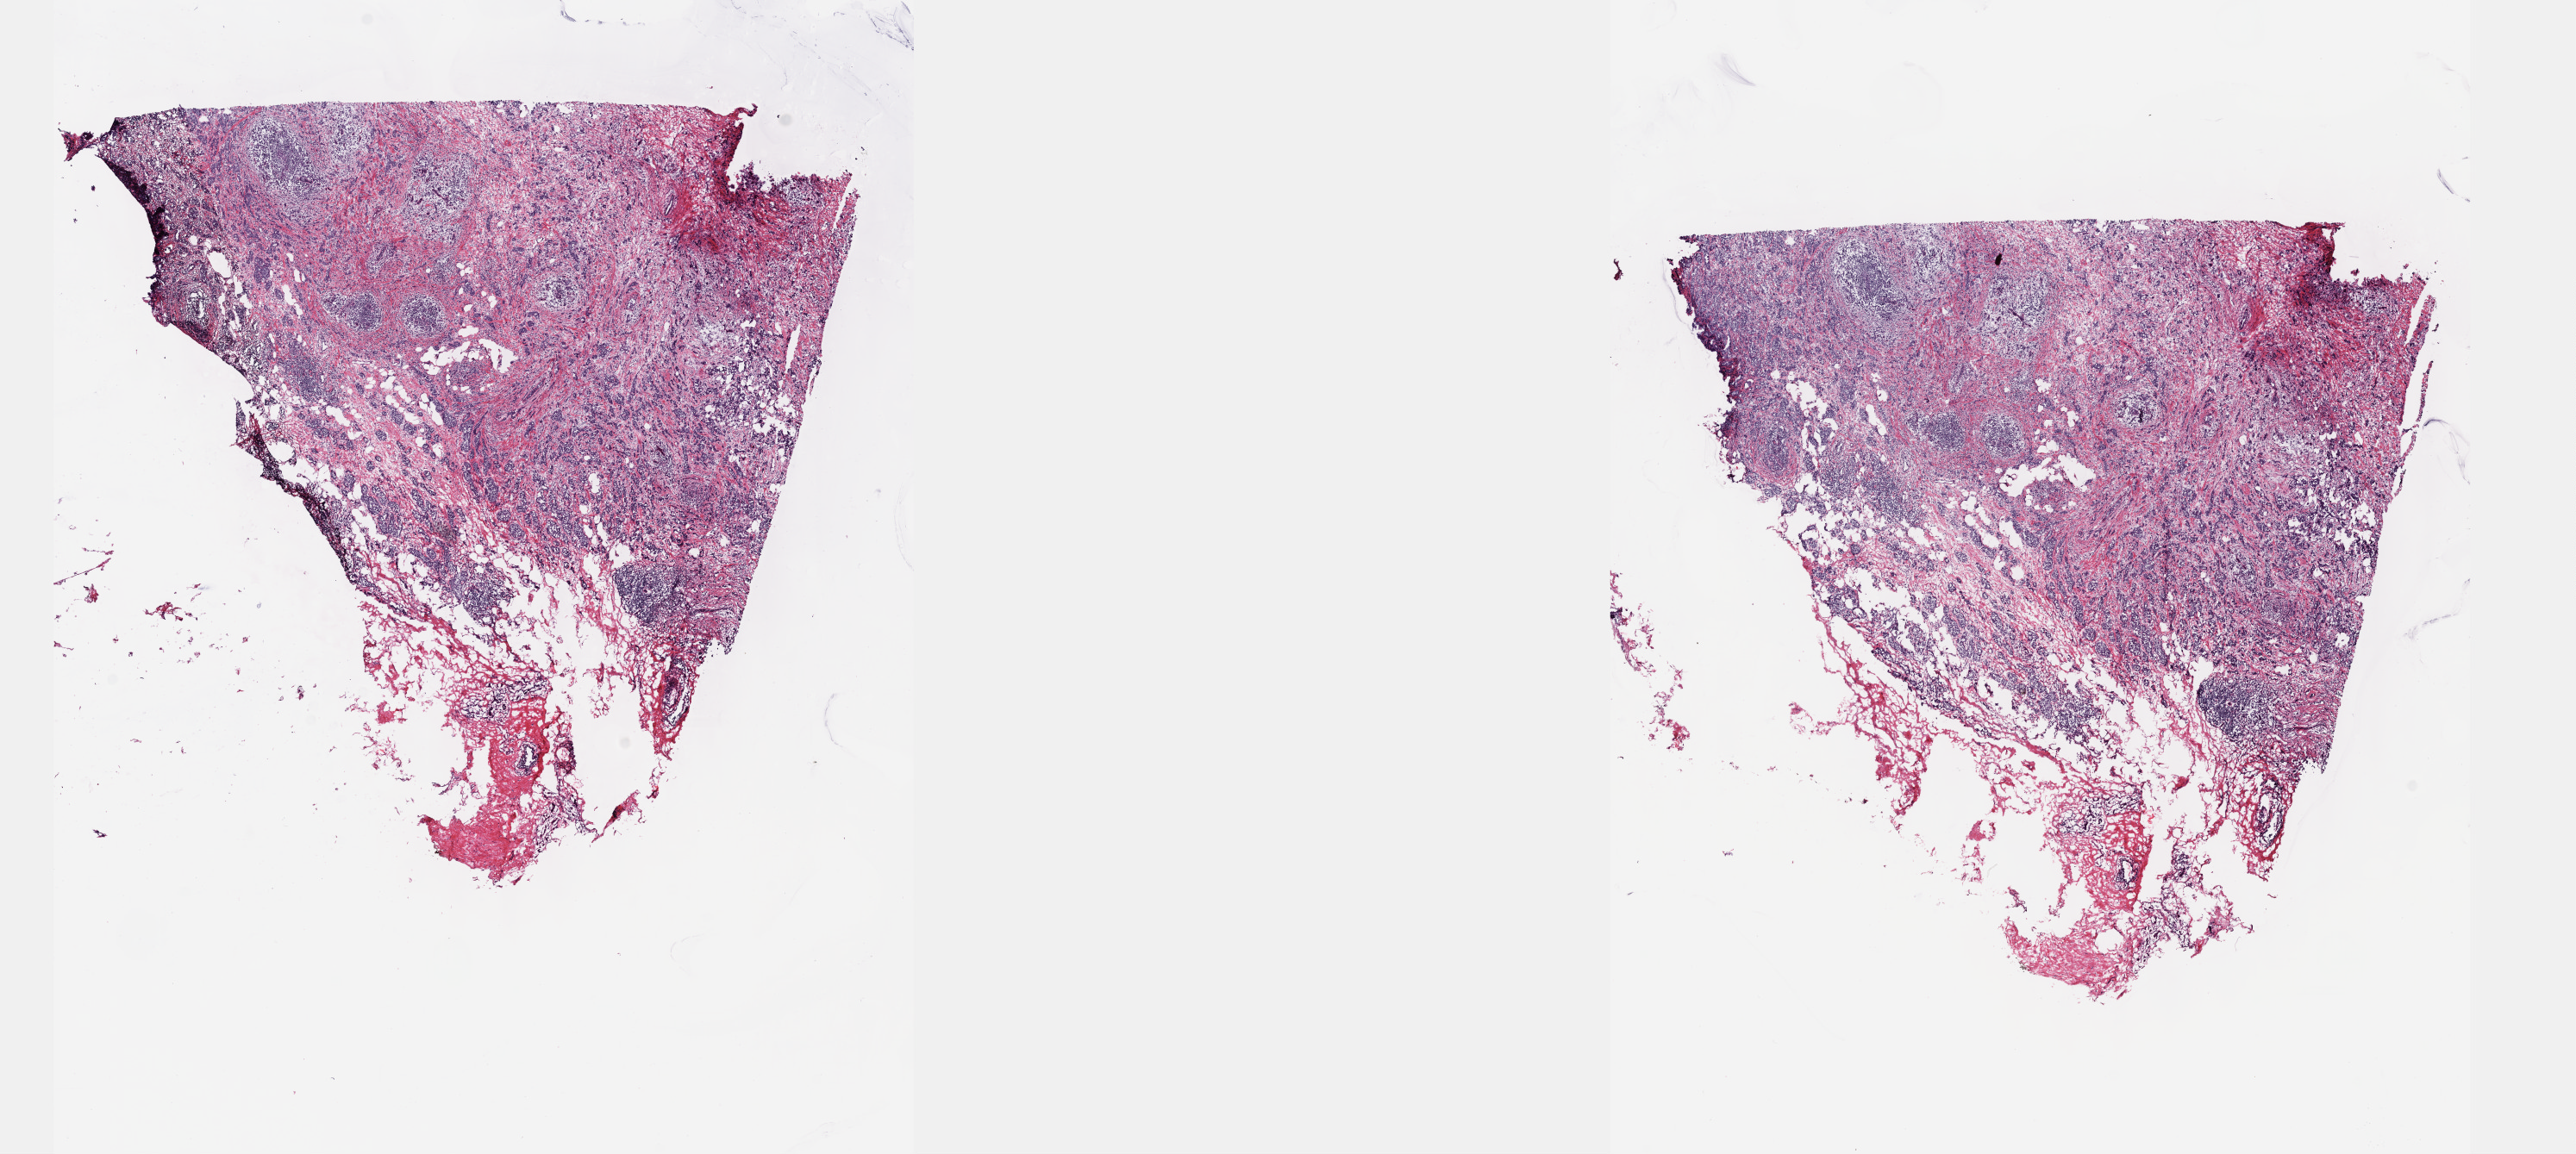
Hematoxylin and eosin (H&E) stained whole-slide image, low-resolution overview of the scanned area, about 24.1 x 10.8 mm (from a 40x scan). Frozen section from the top of the tissue portion. Breast, primary tumour sample. Female, age 52 years at initial diagnosis. Pathologist review of this section (percent, as recorded): tumour cells 60%, tumour nuclei 60%, normal cells 20%, stromal cells 20%, necrosis 0%. Infiltration values recorded for this section: lymphocyte infiltration 10%, monocyte infiltration 0%, neutrophil infiltration 0%.
• lymph nodes positive (case pathology): 23 of 23 examined
• pathologic diagnosis: Infiltrating duct carcinoma, NOS
• AJCC pathologic stage: IIIC (7th edition)
• laterality: left
• TNM: T2 N3a M0